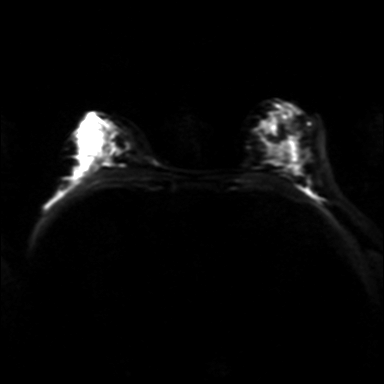
Breast MRI, one axial slice; slice 21 of 36 in the series (ordered by position); diffusion-weighted series; image 2 of 4 stored at this slice position (different b-values; order by instance number); 3 T; 384 × 384 image matrix, field of view 320 × 320 mm. Female patient.
Annotated regions visible in this slice (expert manual segmentation):
- tumour on diffusion-weighted imaging: bounding box (x1, y1, x2, y2) in pixels: (107, 125, 127, 170)